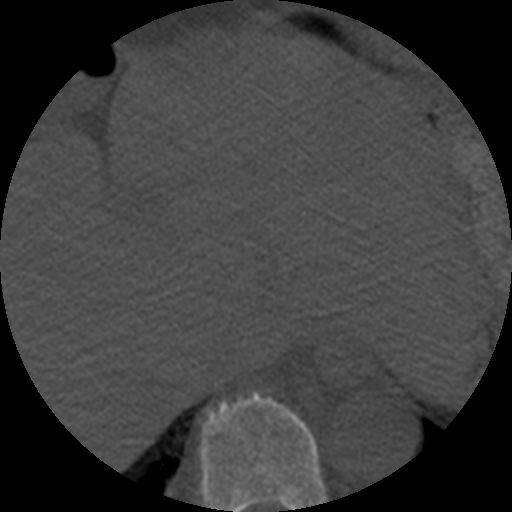
CT including the spine, one axial slice; slice 285 of 508 in the series (ordered by position); reconstruction kernel STANDARD; 120 kVp; bone window (W 1800 / L 400 HU); 1.25 mm slice thickness; 512 × 512 image matrix, field of view 160 × 160 mm. Patient age 57 years. From the clinical record (not read from this slice): primary cancer: prostate.
Annotated regions visible in this slice (semi-automatically segmented with operator editing):
- T9 vertebra: bounding box (x1, y1, x2, y2) in pixels: (199, 391, 327, 512)